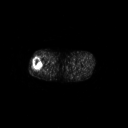
FDG PET of an extremity soft-tissue mass (from a PET/CT study), one axial slice; position 239 of 267 along the scan axis; 3.27 mm slice thickness; 128 × 128 image matrix, field of view 700 × 700 mm. Male patient, age 43 years. From the clinical record (not read from this slice): histological type: poorly differentiated synovial sarcoma; grade: high; site of the primary tumour: right buttock.
Annotated regions visible in this slice (expert contour drawn on MRI and transferred to this co-registered scan by the dataset authors):
- gross tumour volume including surrounding oedema: bounding box <31,58,43,71> (left, top, right, bottom; pixels)
- gross tumour volume (mass): <33,58,43,71>